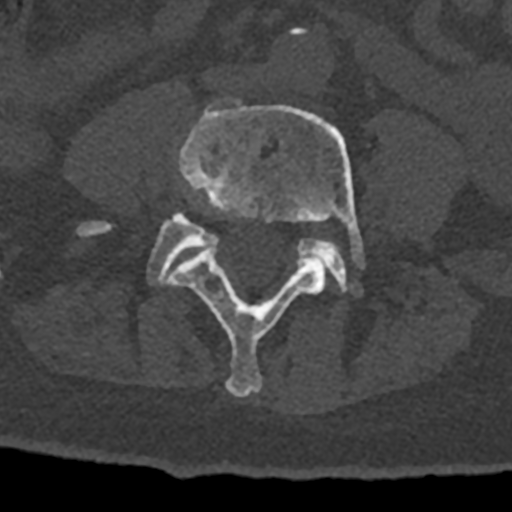
CT including the spine, one axial slice; position 241 of 797 along the scan axis; reconstruction kernel Br40s/3; 120 kVp; bone window (W 1800 / L 400 HU); 0.5 mm slice thickness; 512 × 512 image matrix, field of view 160 × 160 mm. Patient: male, 74 years. Case-level facts recorded for this patient, not image findings: primary cancer: renal; vertebrae with lytic lesions (as recorded): T10, L1, L2, L3, L4, L5.
Outlined on this slice (semi-automatic segmentation, software-assisted and operator-edited):
- L4 vertebra: bounding box (x1, y1, x2, y2) in pixels: (167, 104, 364, 397)
- L5 vertebra: (78, 214, 350, 290)